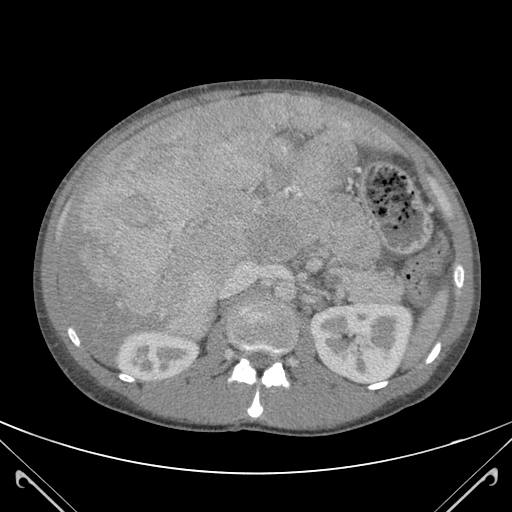
Contrast-enhanced abdominal CT (liver protocol), one axial slice. Slice 68 of 118 in the series (ordered by position). 120 kVp. Soft-tissue window (W 400 / L 40 HU). 3 mm slice thickness. 512 × 512 image matrix, field of view 380 × 380 mm. Case-level facts recorded for this patient, not image findings: diagnosis: hepatocellular carcinoma (patient treated with transarterial chemoembolisation; whether this scan precedes or follows treatment is not stated here); TNM stage (as recorded): Stage-IIIB; Child-Pugh class: A.
Structures marked on this image (semi-automatic segmentation, software-assisted and operator-edited):
- abdominal aorta: bounding box <275,279,297,302> (left, top, right, bottom; pixels)
- liver parenchyma outside the tumour (the mass and vessels are separate outlines, so this box may not span the whole liver): <58,94,376,359>
- mass: <63,96,368,337>
- liver vessels: <220,168,358,299>